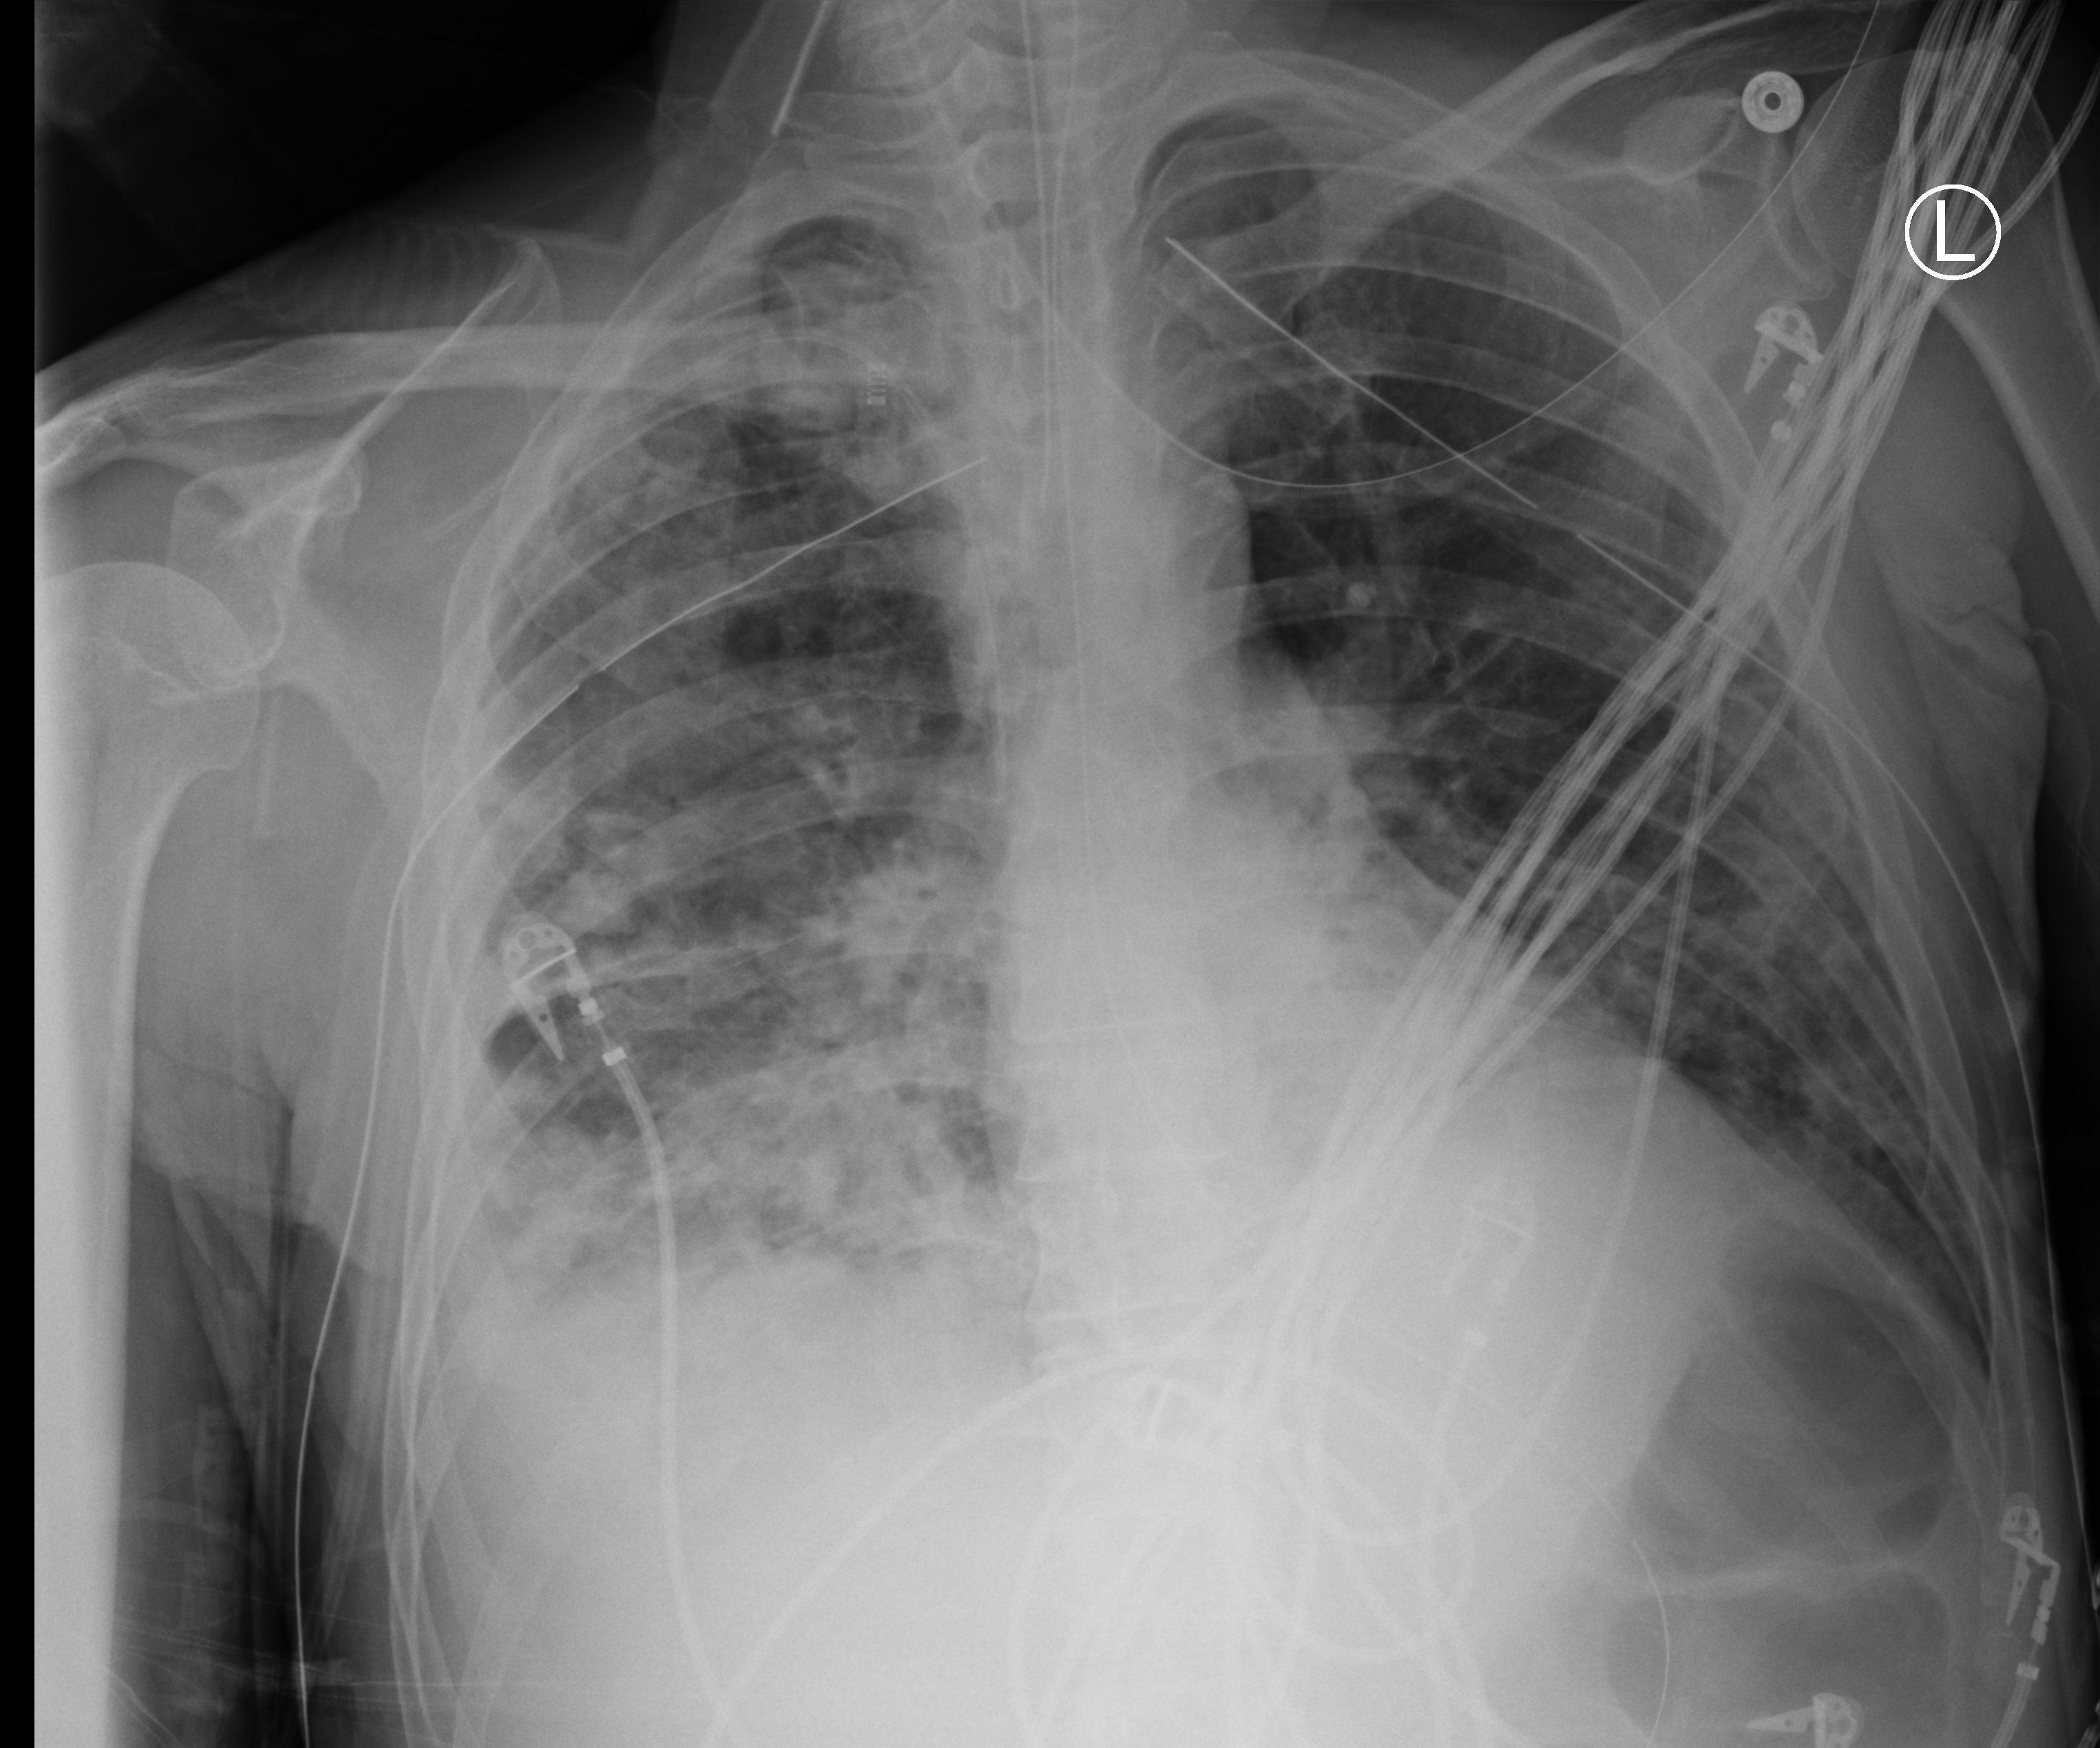
Bedside chest radiograph (computed radiography); anteroposterior (AP) projection. Male patient hospitalised with COVID-19, age 18–59 years.
Hospital-stay facts (about this admission, not read from this image; timing relative to this image not recorded): mechanically ventilated during this hospital stay: yes; admitted to intensive care during this hospital stay: yes.